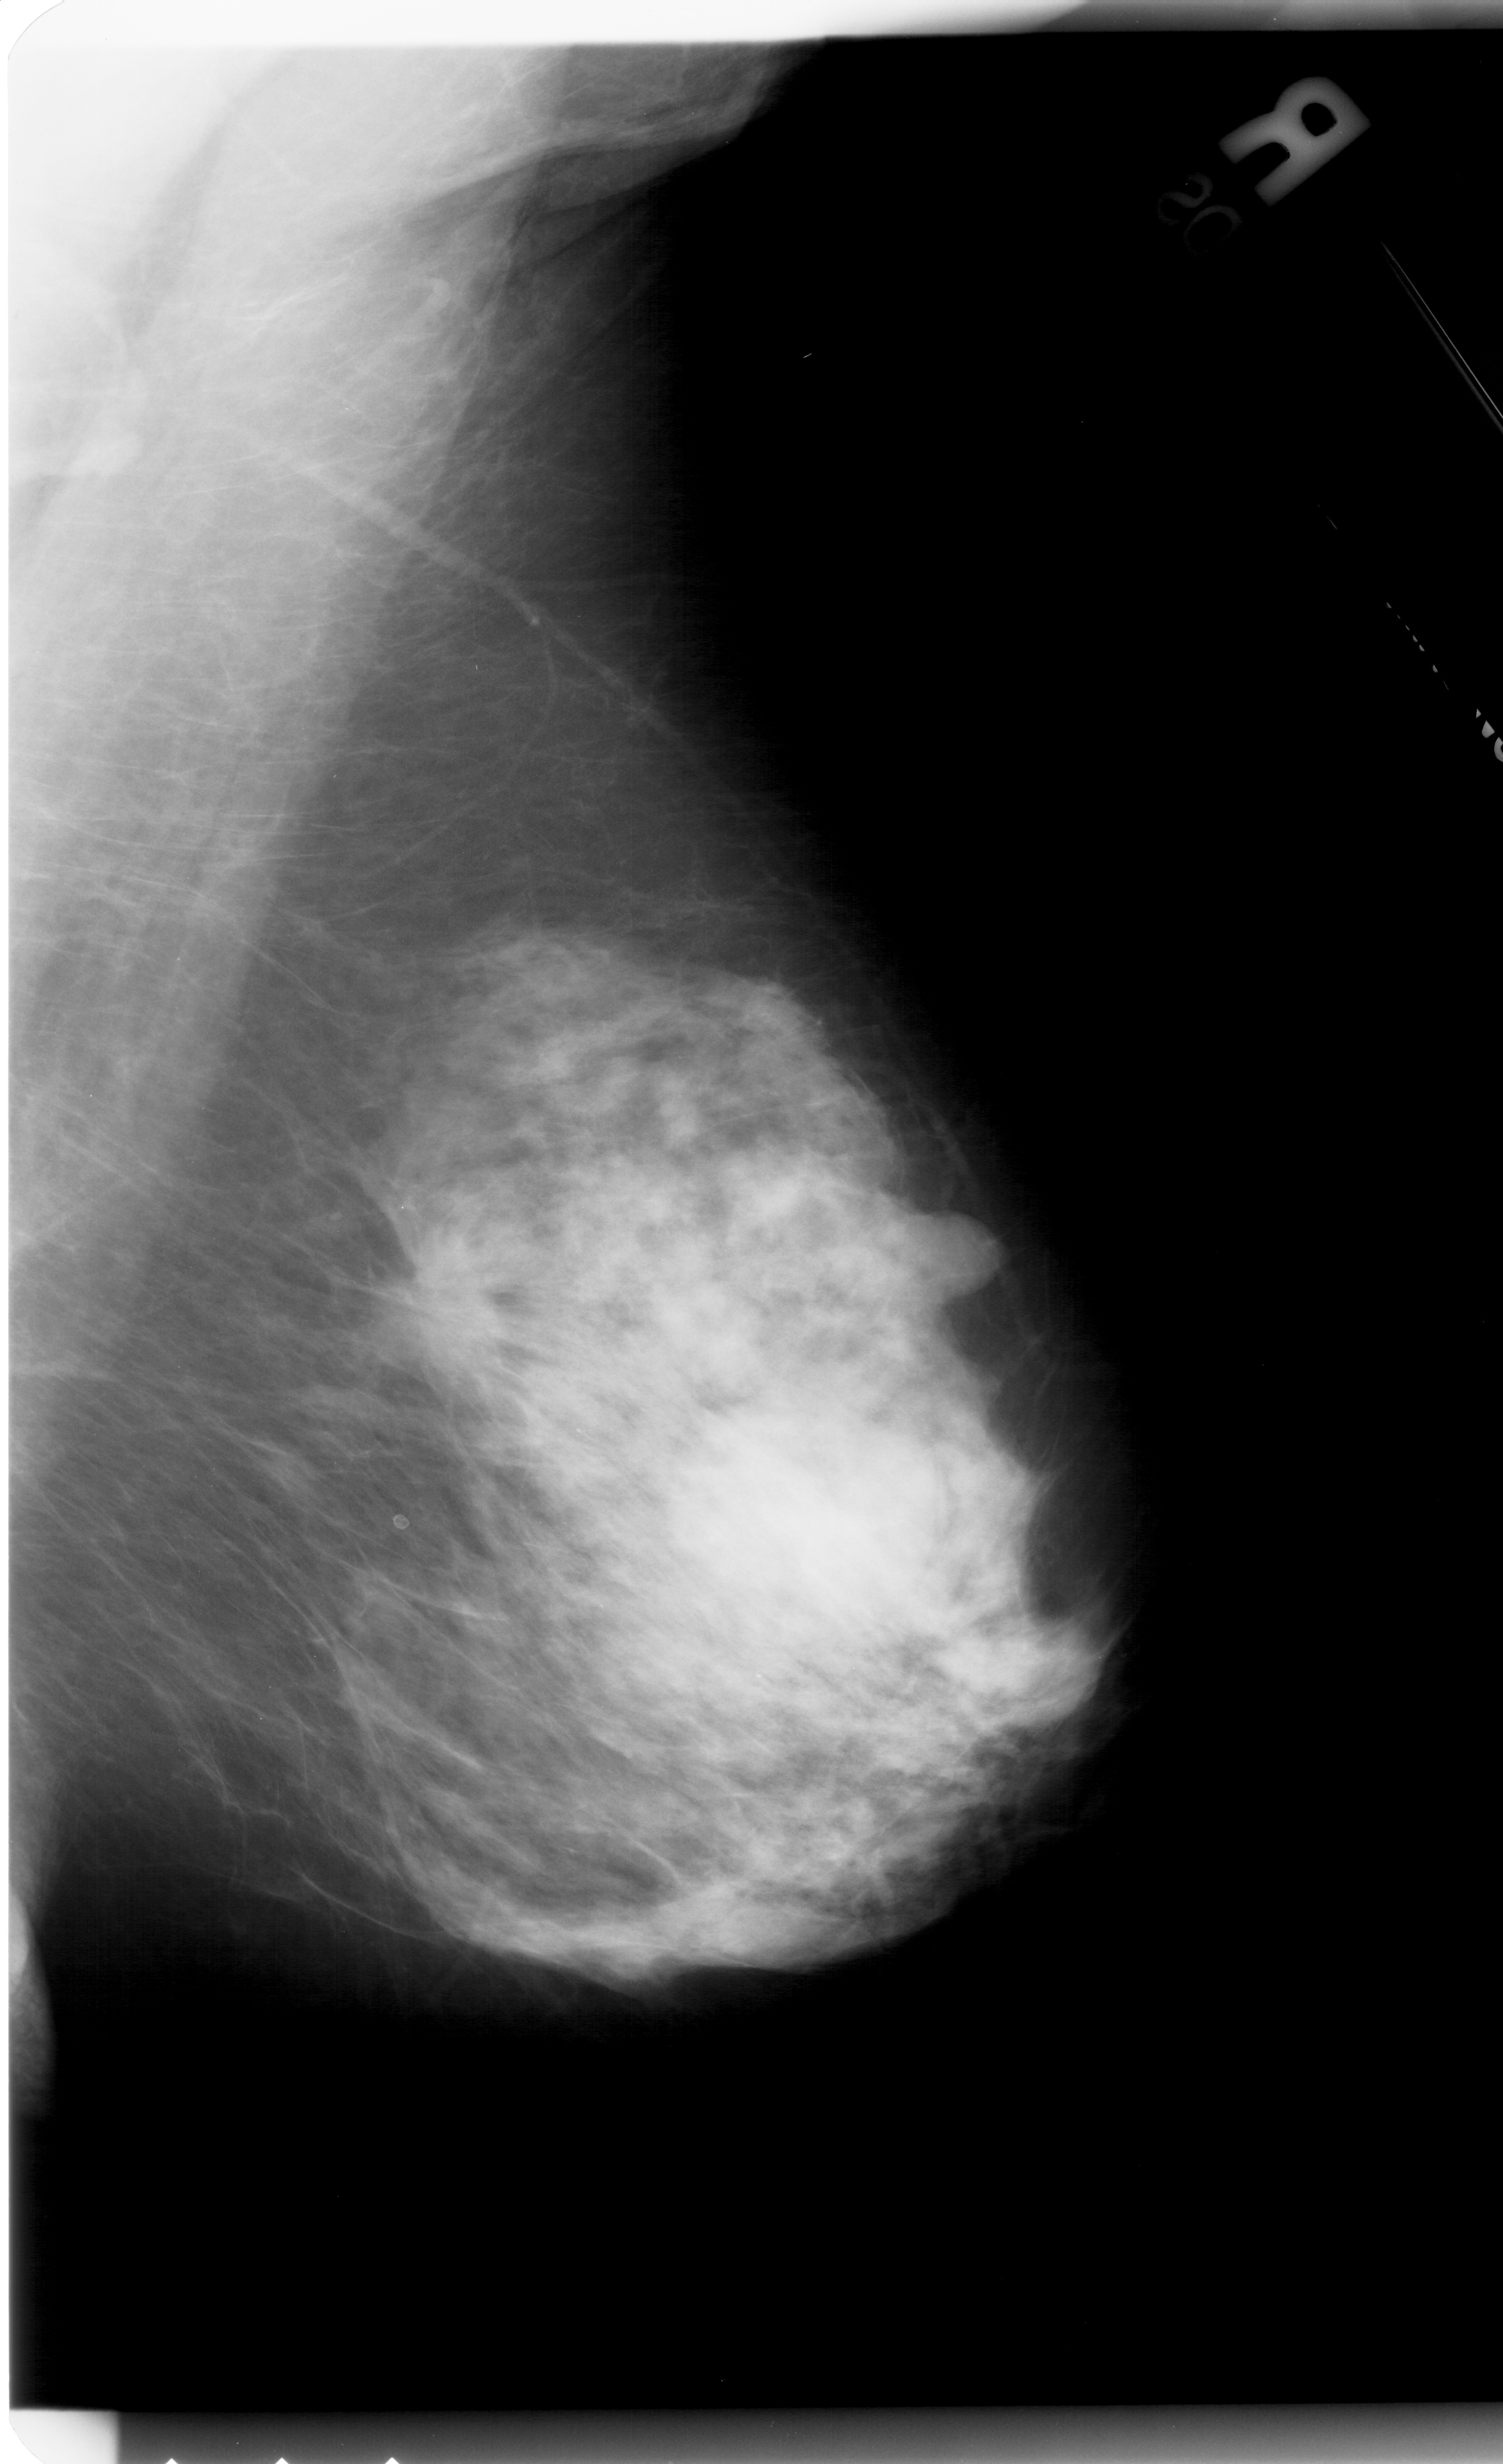
Mammogram (digitized film); right breast; MLO view; breast composition: extremely dense (BI-RADS density category 4 of 4).
Abnormality record for this image: mass, shape irregular, margins spiculated; BI-RADS assessment category 5; subtlety rating 4 on a 1 (subtle) to 5 (obvious) scale; pathology result (as recorded, not read from the image): malignant.